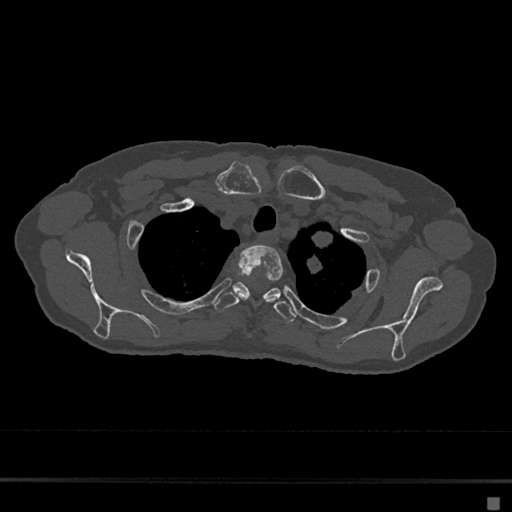
CT including the spine, one axial slice; slice 560 of 797 in the series (ordered by position); 120 kVp; bone window (W 1800 / L 400 HU); 0.5 mm slice thickness; 512 × 512 image matrix. Patient: female, 68 years. From the clinical record (not read from this slice): primary cancer: renal.
Structures marked on this image (semi-automatic segmentation, software-assisted and operator-edited):
- T2 vertebra: box from (x=236, y=245) to (x=283, y=303) px
- T3 vertebra: (x=213, y=282)–(x=296, y=323)